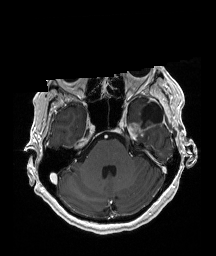
Brain MRI from a brain-tumour surgery series, one axial slice; T1-weighted post-contrast; 1 mm slice thickness; 216 × 256 image matrix, field of view 211 × 250 mm. Case-level facts recorded for this patient, not image findings: histopathology: Glioblastoma; WHO grade: 4; IDH mutation: no; tumour location: Left Temporal.
Outlined on this slice (outlined manually by an expert reader):
- previous resection cavity: bounding box [x1, y1, x2, y2] px = [141, 103, 162, 124]